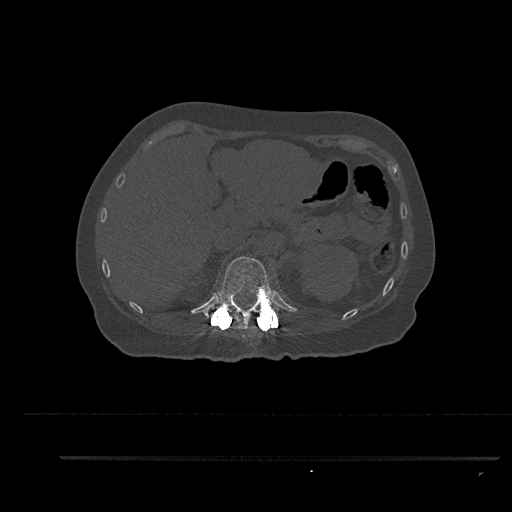
CT including the spine, one axial slice; position 265 of 797 along the scan axis; reconstruction kernel Br40s/3; bone window (W 1800 / L 400 HU); 0.5 mm slice thickness; 512 × 512 image matrix, field of view 408 × 408 mm. Patient: female, 44 years. From the clinical record (not read from this slice): primary cancer: renal.
Outlined on this slice (semi-automatically segmented with operator editing):
- T12 vertebra: bounding box <207,255,281,329> (left, top, right, bottom; pixels)